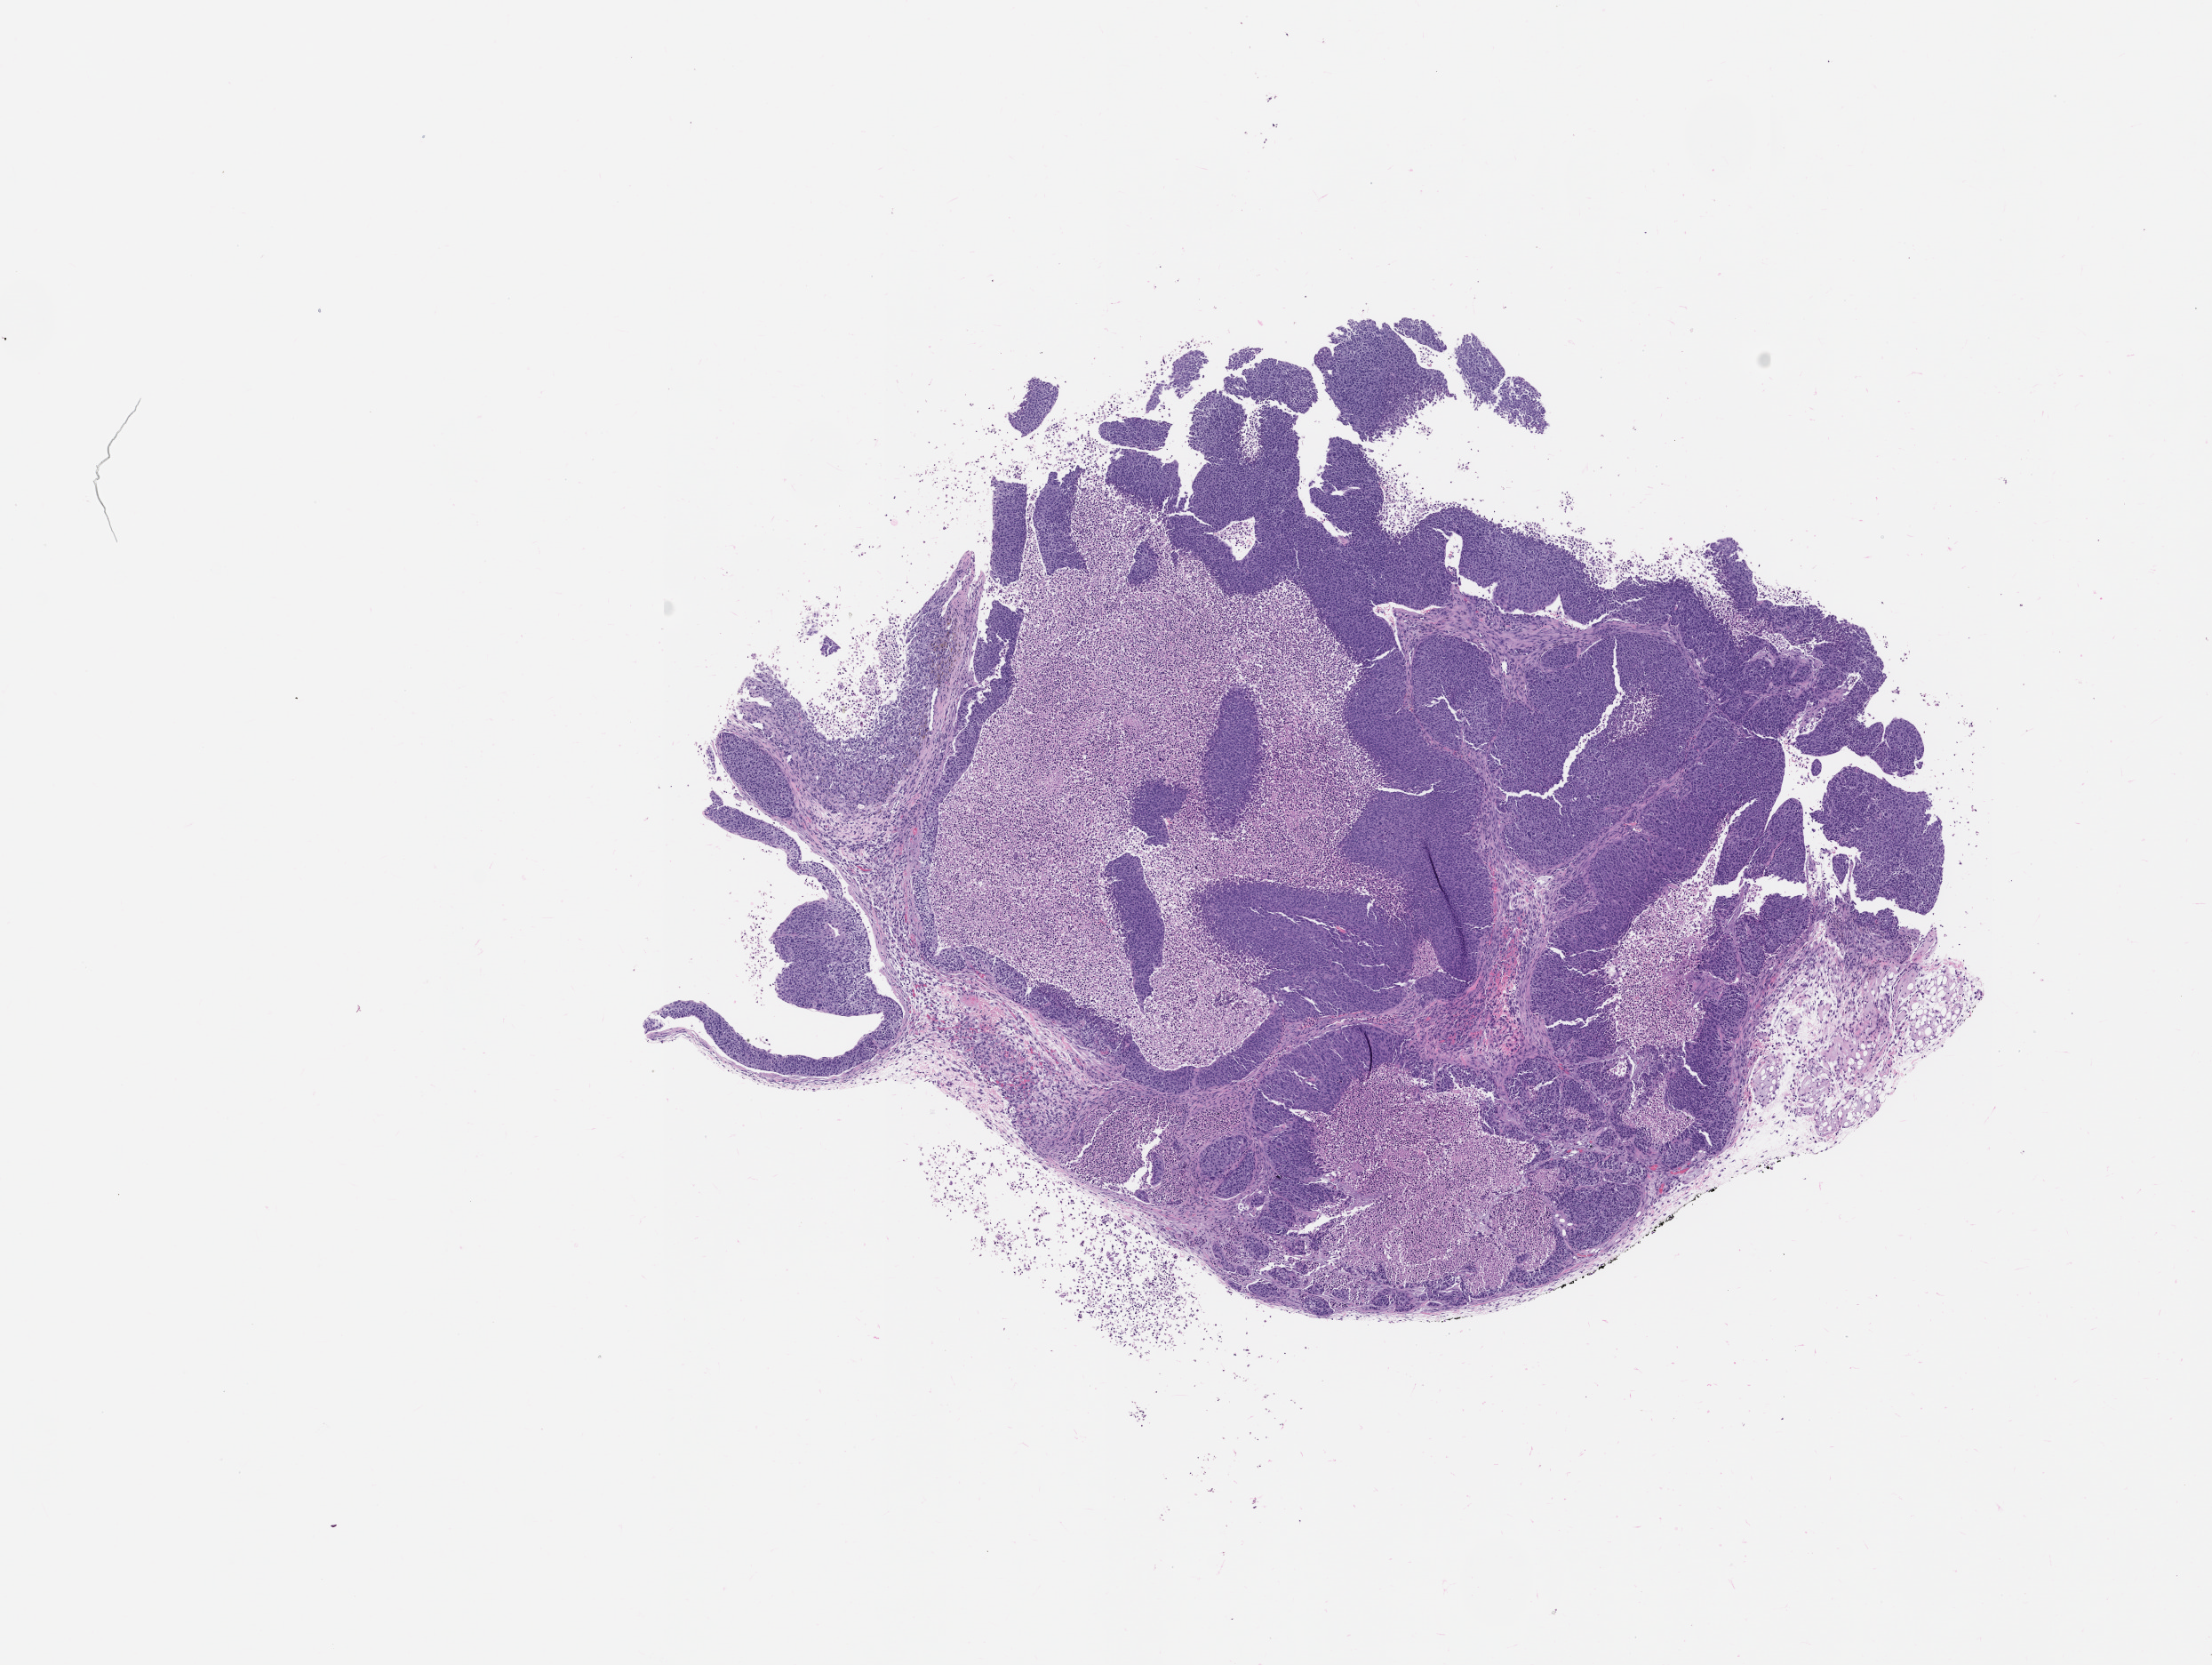
Hematoxylin and eosin (H&E) whole-slide image of a patient-derived xenograft (PDX) tumor grown in a mouse, passage 1 — shown as a low-resolution overview of the whole scanned area (about 10.0 x 7.5 mm); formalin-fixed, paraffin-embedded (FFPE) tissue; tumor site category: head and neck.
Originating patient diagnosis: Head and Neck Squamous Cell Carcinoma.